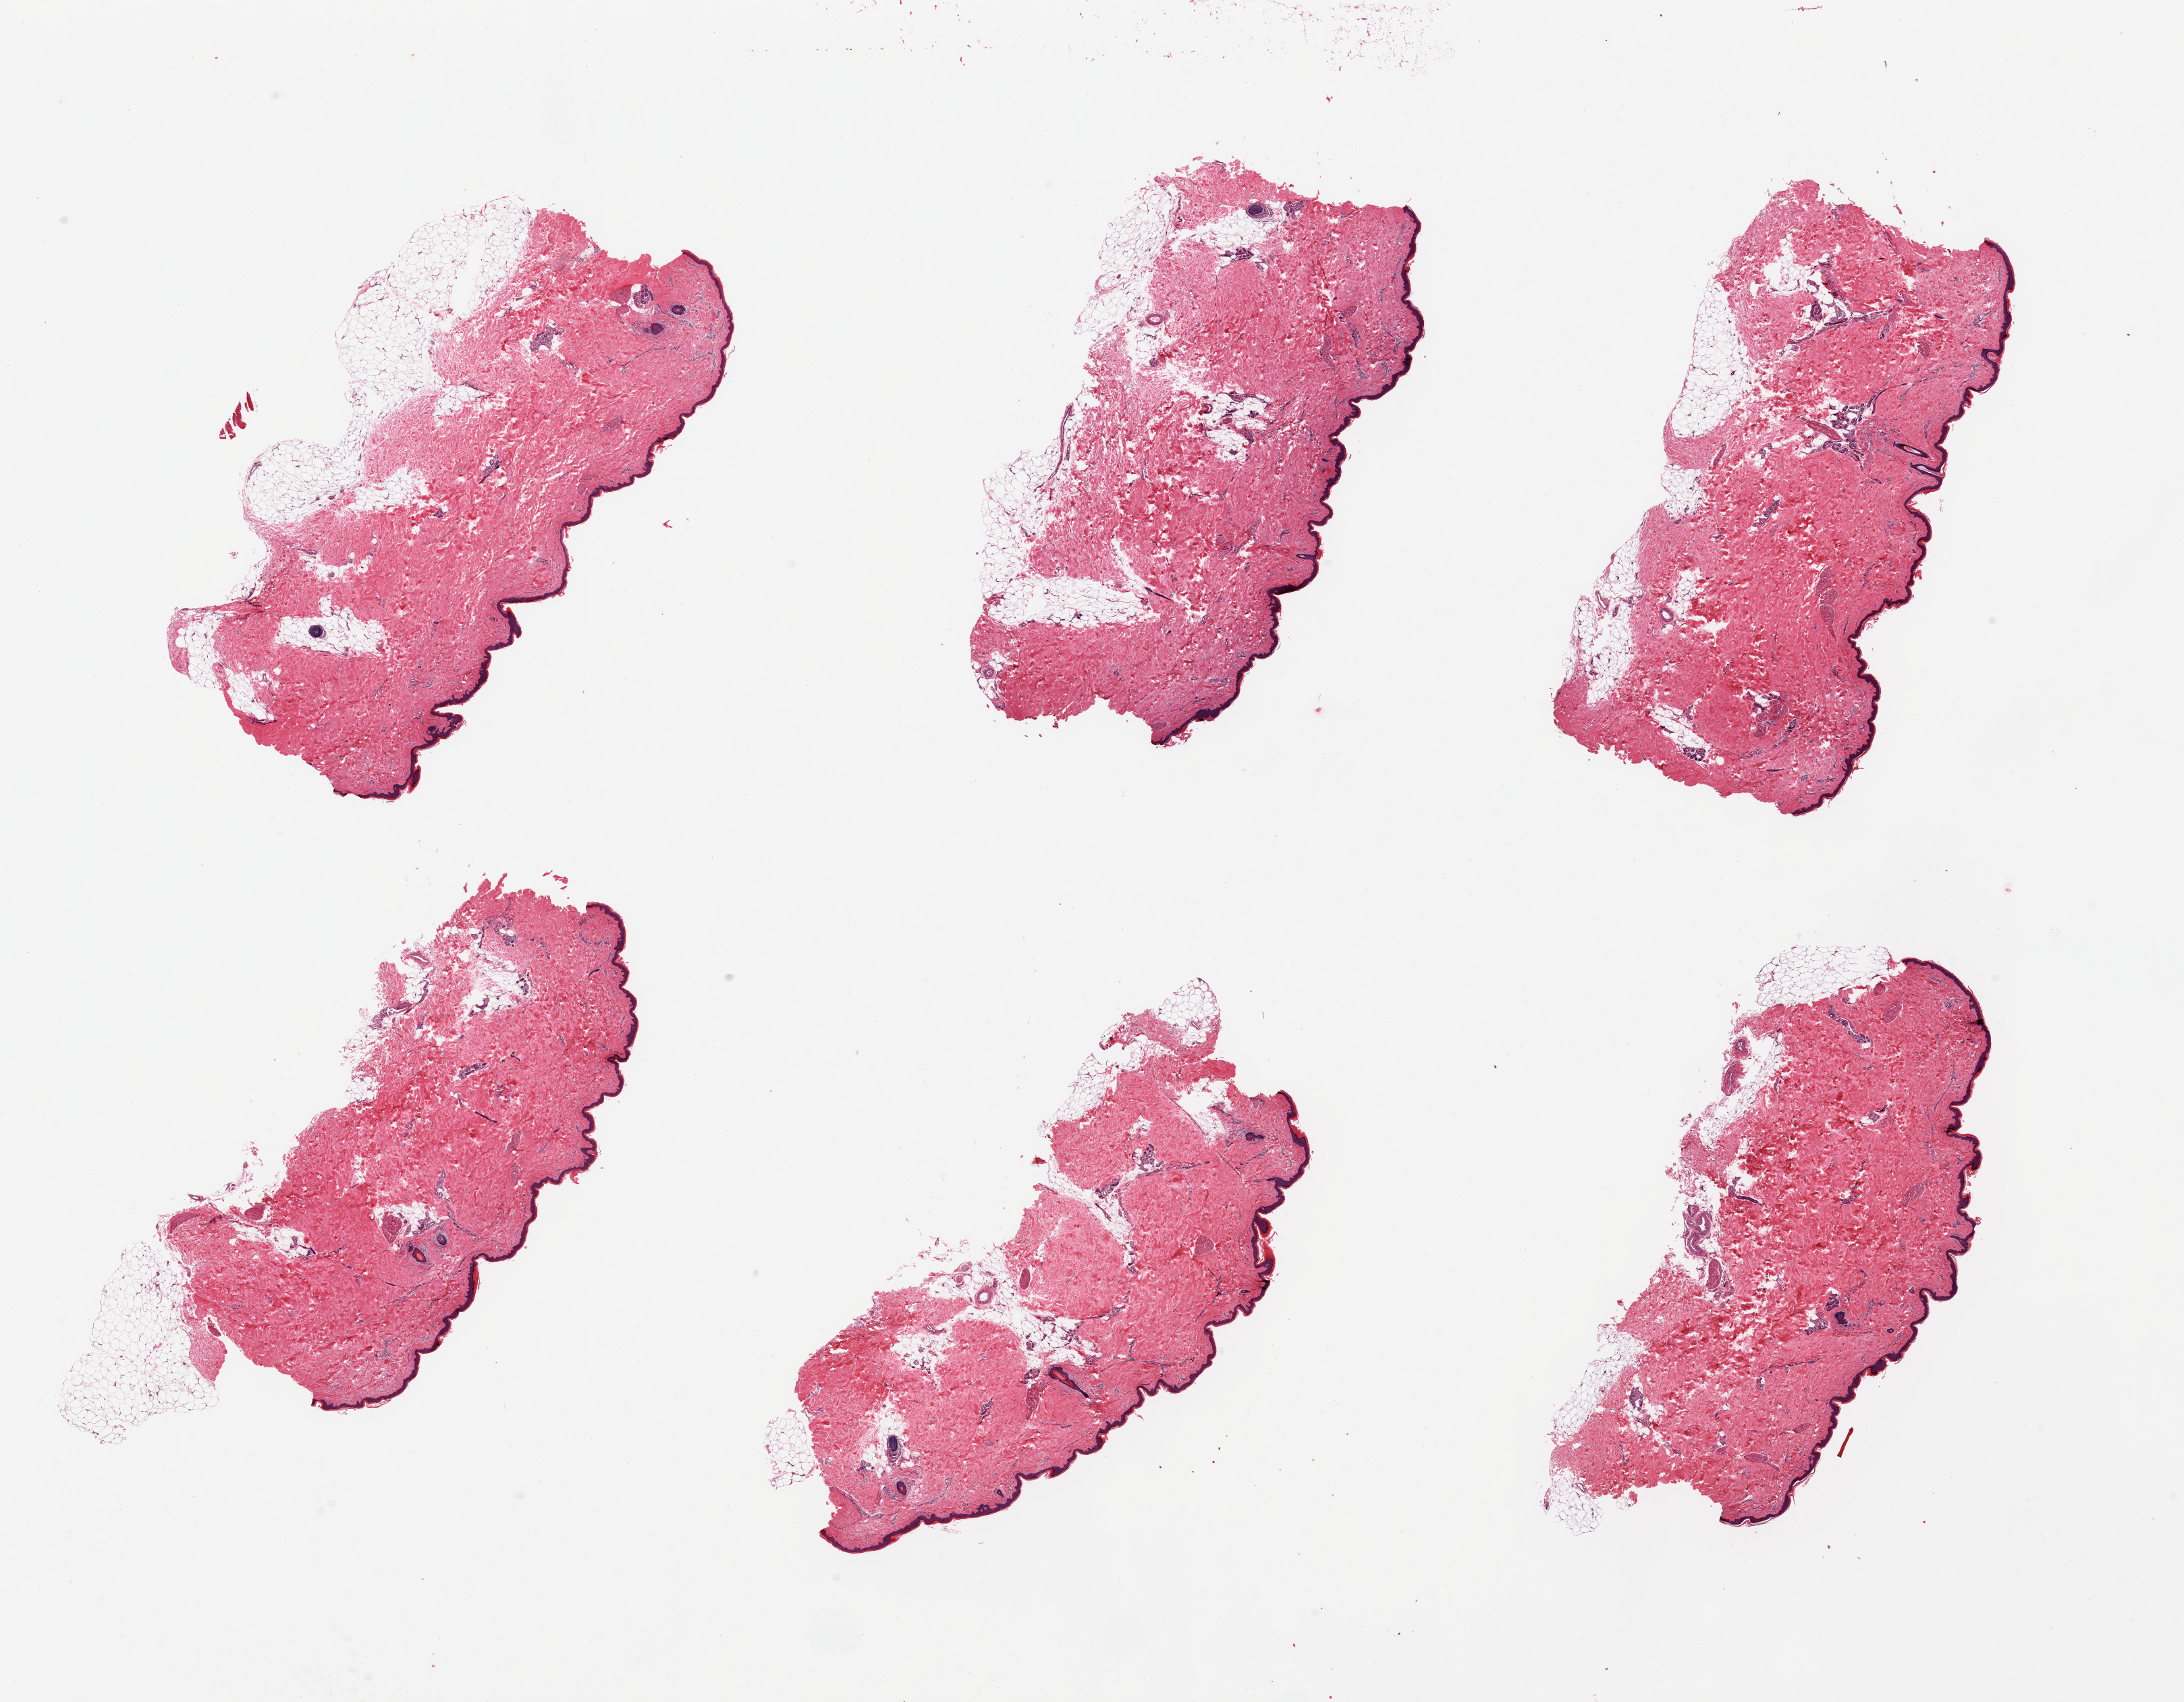
H&E whole-slide image, shown as a low-resolution overview of the whole scanned area (about 25.6 x 19.9 mm, slide scanned at 20x), PAXgene-fixed, paraffin-embedded tissue, target tissue: skin of lower leg, tissue donor sample. Female donor.
• review note (as recorded): 6 pieces, focal adherent dermal fat up to ~1mm